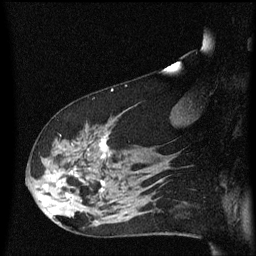
Breast MRI (dynamic contrast-enhanced), one sagittal slice; dynamic contrast-enhanced series, image 2 of 3 at this slice position (ordered by acquisition); 1.5 T; TE 4.2 ms, TR 8.4 ms; 2 mm slice thickness; 256 × 256 image matrix, field of view 200 × 200 mm. Female patient, age 48 years.
Outlined on this slice (semi-automatically segmented with operator editing):
- analysis volume of interest (the breast-tissue region the enhancement analysis was run in; not a lesion): bounding box (x1, y1, x2, y2) in pixels: (31, 116, 134, 225)
- tumour enhancement mask (voxels above the 70 % enhancement threshold inside the analysis volume of interest): (40, 136, 107, 205)